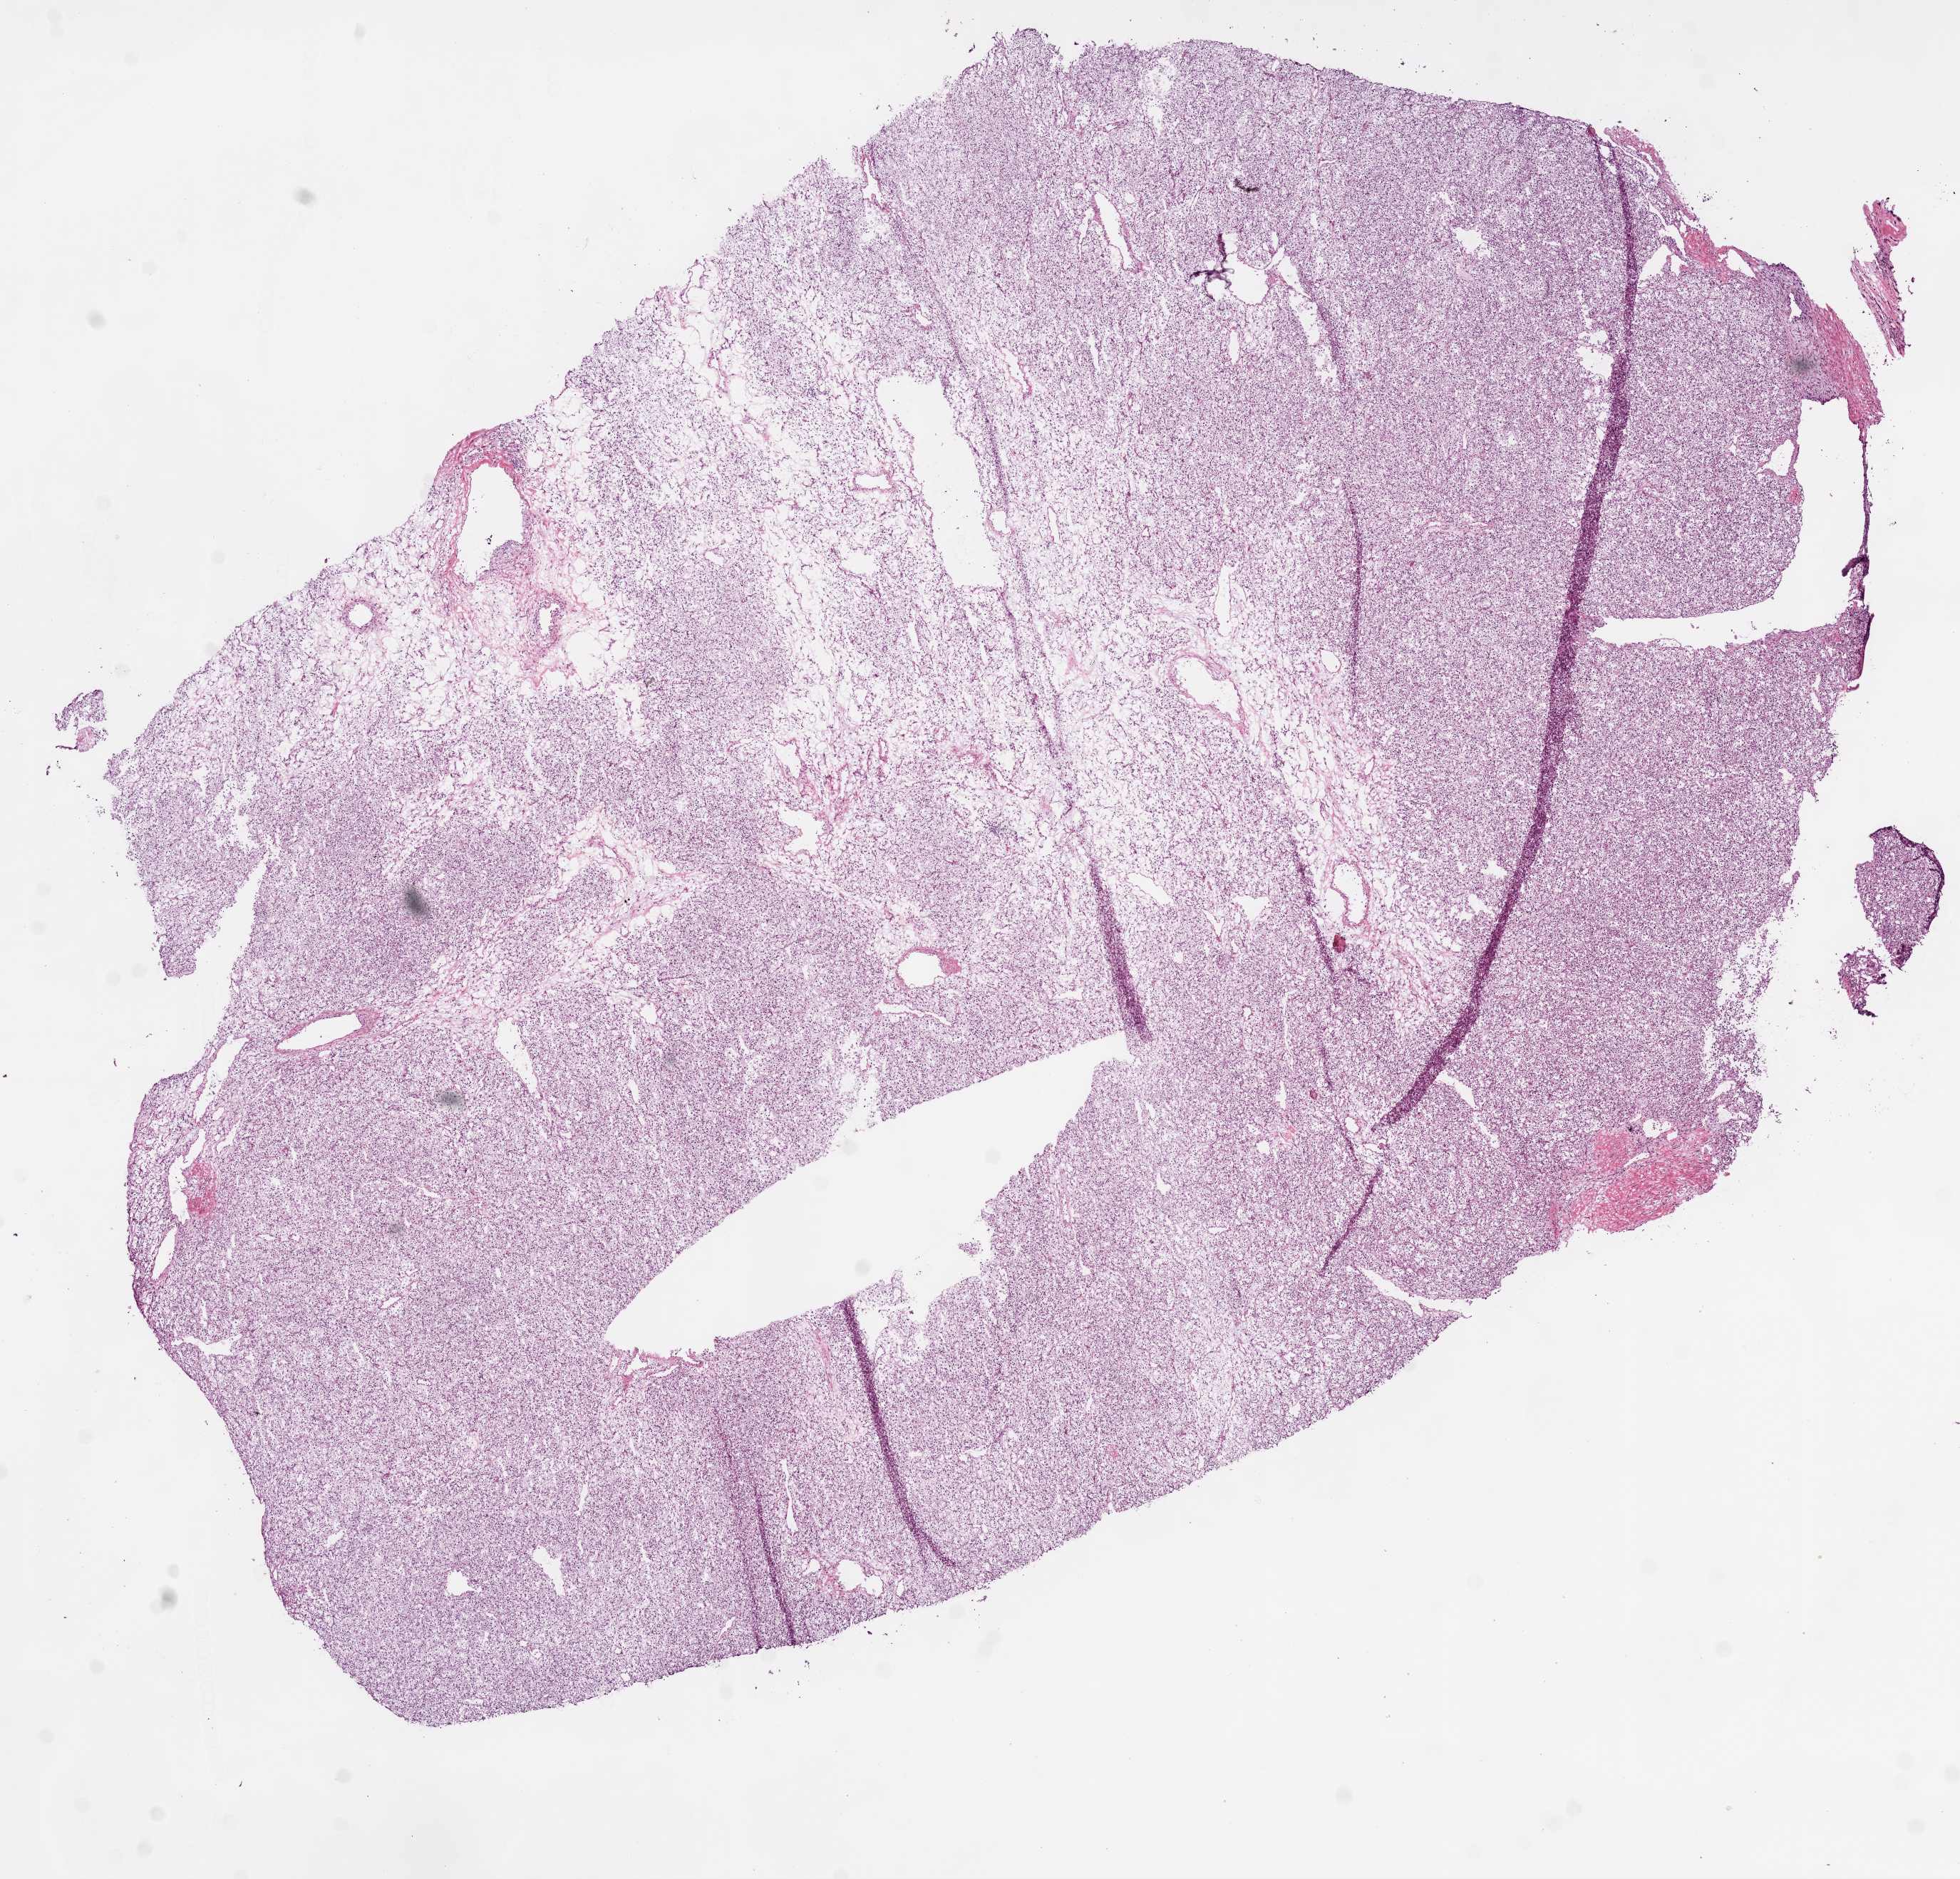
H&E-stained whole-slide image — whole scanned area (about 11.0 x 10.6 mm) shown as a low-resolution overview, frozen section, kidney, primary tumour sample. Patient: male, age at initial diagnosis 50 years. Histologic grade: G2 (moderately differentiated). Composition of this section per pathologist review: tumour cells 100%, tumour nuclei 90%, necrosis 0%. Inflammatory infiltration, as recorded: lymphocyte infiltration 2%.
AJCC pathologic stage: I. Laterality: left. Pathologic diagnosis: Clear cell adenocarcinoma, NOS.